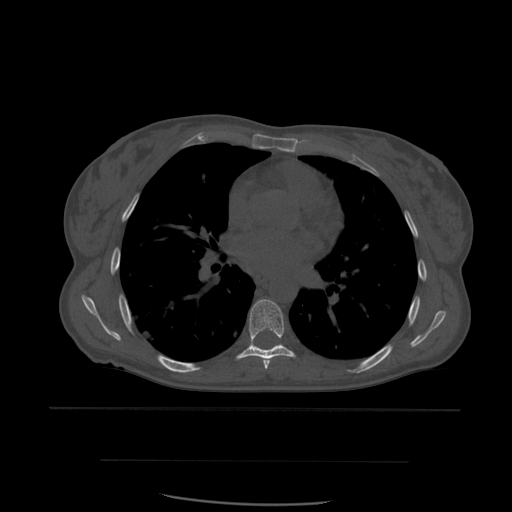
CT including the spine, one axial slice. Slice 376 of 574 in the series (ordered by position). Bone window (W 1800 / L 400 HU). 1.25 mm slice thickness. 512 × 512 image matrix, field of view 392 × 392 mm. Patient age 48 years. Case-level facts recorded for this patient, not image findings: primary cancer: lung; vertebrae with lytic lesions (as recorded): T11.
Annotated regions visible in this slice (semi-automatic segmentation, software-assisted and operator-edited):
- T6 vertebra: bounding box [x1, y1, x2, y2] px = [263, 359, 270, 370]
- T7 vertebra: [237, 299, 296, 361]